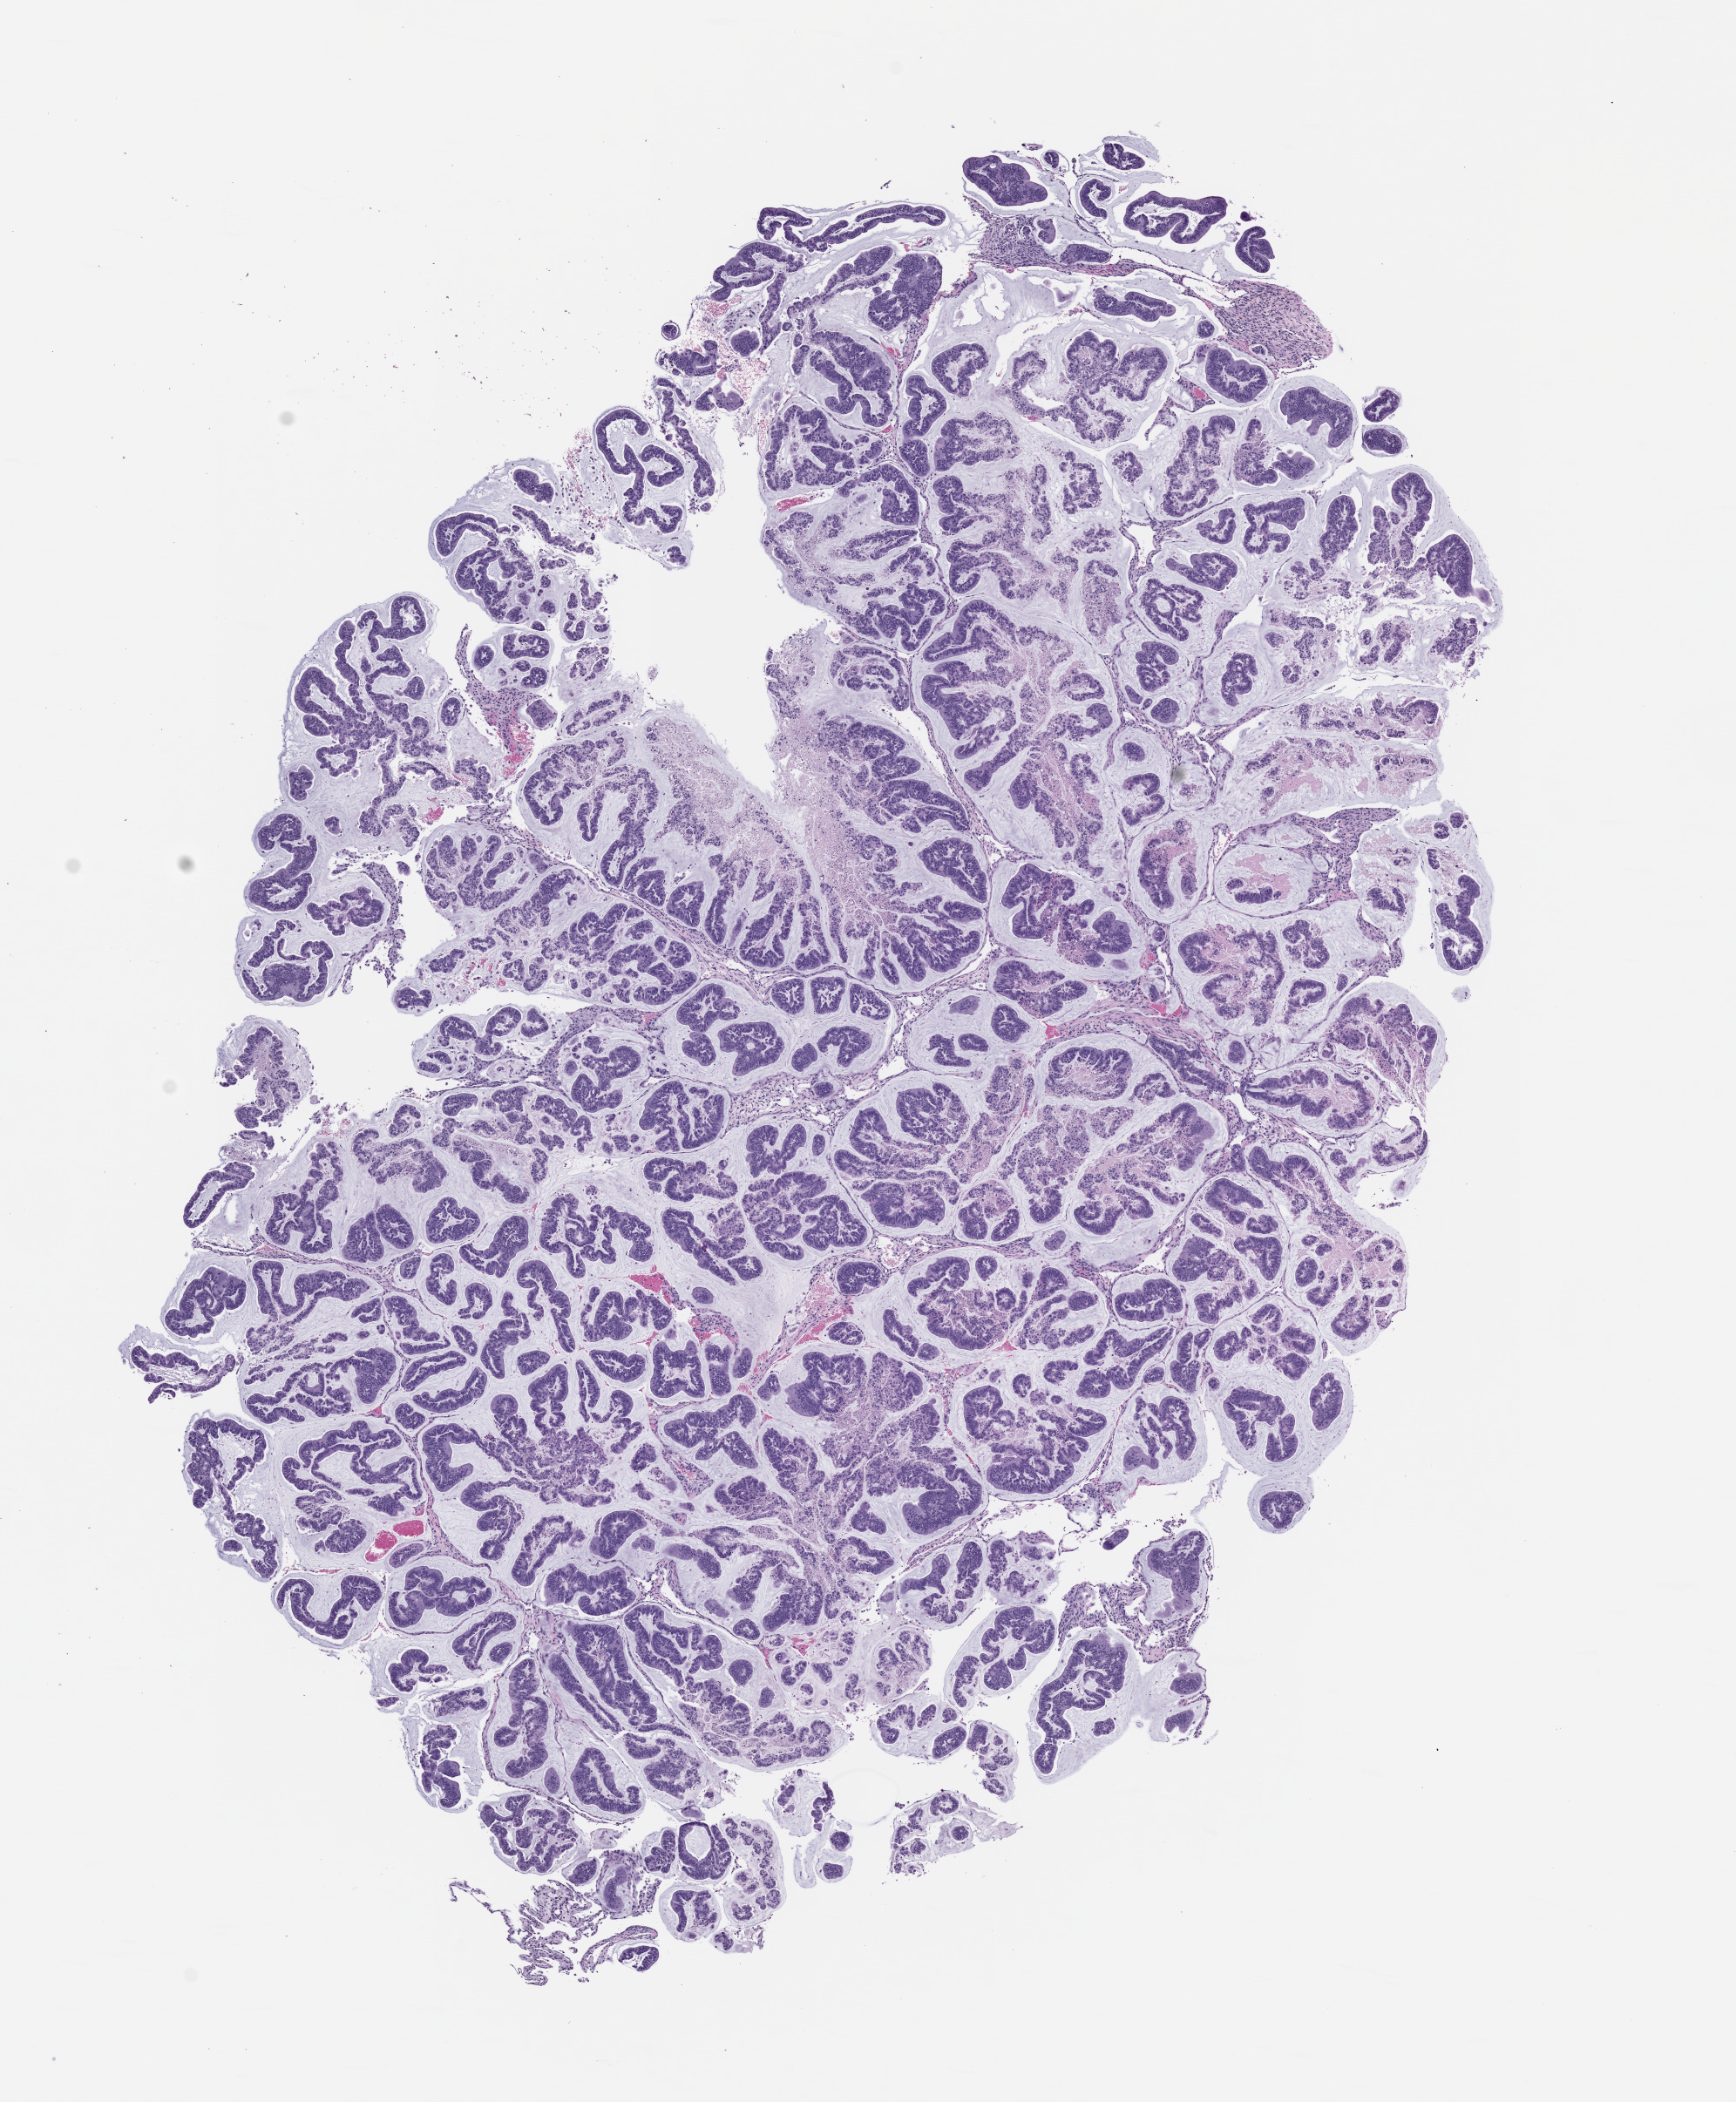
Haematoxylin and eosin whole-slide image of a patient-derived xenograft (PDX) tumor grown in a mouse, passage 2, a low-resolution overview of the entire scanned area, about 8.0 x 9.7 mm, formalin-fixed paraffin-embedded section, originating tumor site category: colon.
Originating patient diagnosis: Colon Adenocarcinoma.